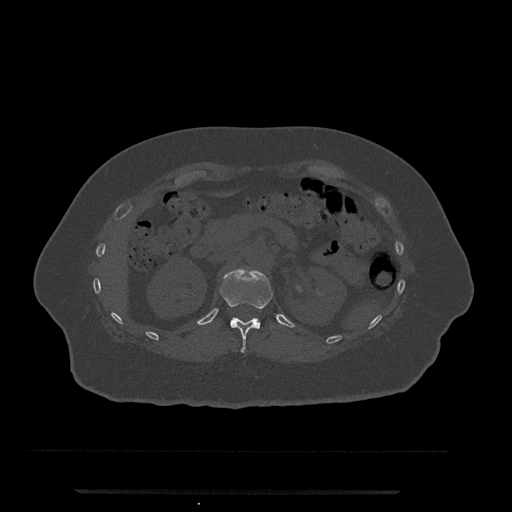
CT including the spine, one axial slice; position 159 of 797 along the scan axis; reconstruction kernel Br40s/3; bone window (W 1800 / L 400 HU); 0.5 mm slice thickness; 512 × 512 image matrix. Female patient, age 51 years. From the clinical record (not read from this slice): primary cancer: neuro; vertebrae with lytic lesions (as recorded): T8.
Structures marked on this image (semi-automatically segmented with operator editing):
- T12 vertebra: bounding box <220,267,273,353> (left, top, right, bottom; pixels)